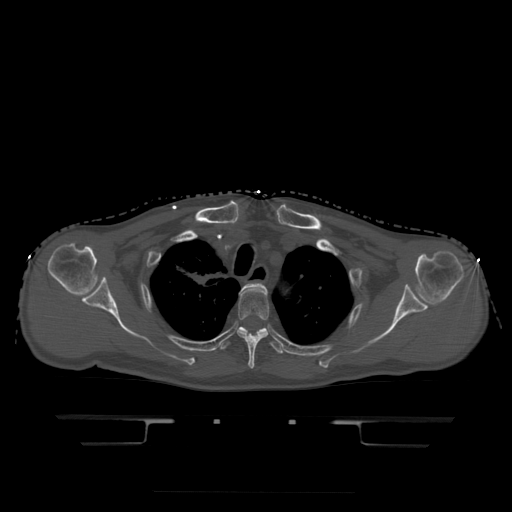
CT including the spine, one axial slice. Slice 367 of 522 in the series (ordered by position). Bone window (W 1800 / L 400 HU). 512 × 512 image matrix. Patient age 68 years. From the clinical record (not read from this slice): primary cancer: urothelial.
Structures marked on this image (semi-automatic segmentation, software-assisted and operator-edited):
- T2 vertebra: bounding box [x1, y1, x2, y2] px = [244, 284, 263, 289]
- T3 vertebra: [237, 284, 269, 369]
- T4 vertebra: [219, 327, 284, 354]